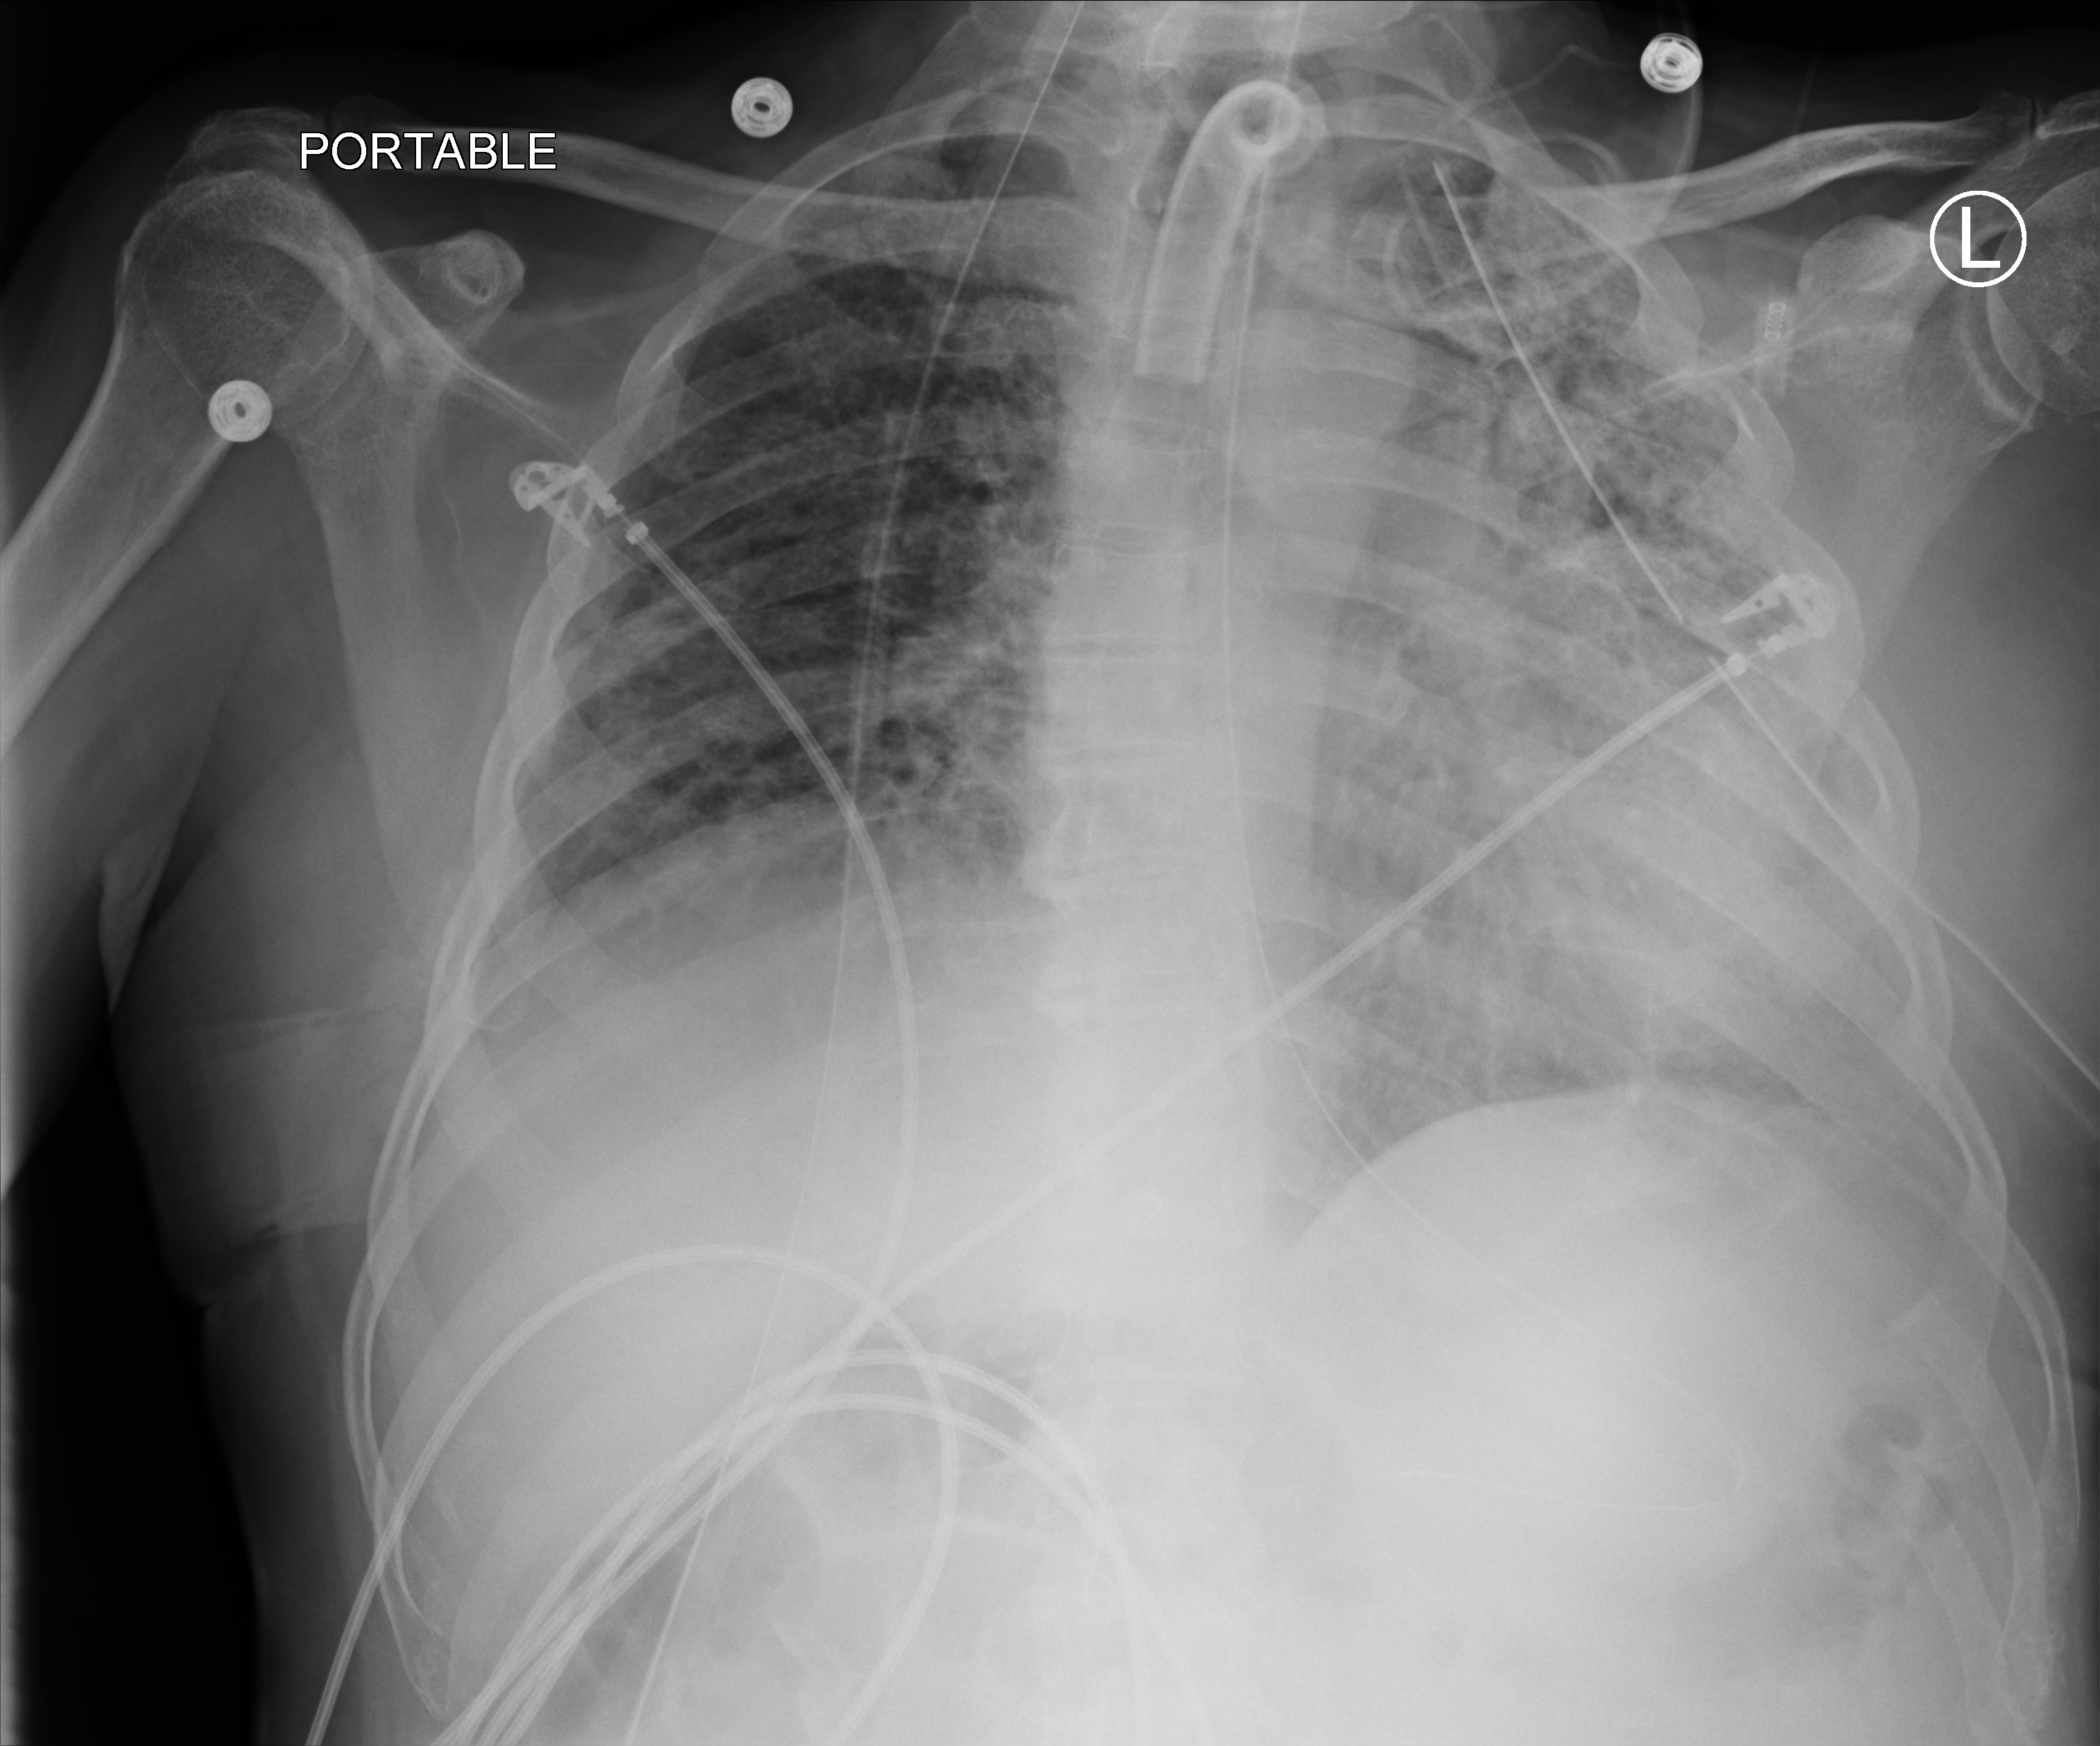
Portable chest radiograph; anteroposterior (AP) projection. Patient hospitalised with COVID-19; male, aged 18–59 years.
Admission-level facts for this patient (not findings on this image; timing relative to this image not recorded): length of hospital stay: 83 days; chronic kidney disease (admission record): no.